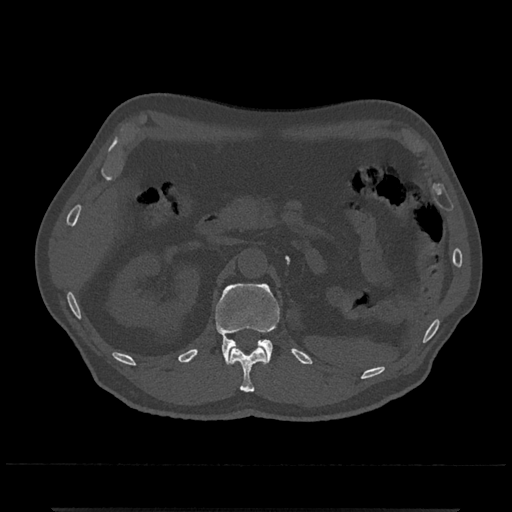
CT including the spine, one axial slice; slice 390 of 797 in the series (ordered by position); reconstruction kernel Br40s/3; 120 kVp; bone window (W 1800 / L 400 HU); 512 × 512 image matrix. Male patient, age 67 years. Case-level facts recorded for this patient, not image findings: primary cancer: prostate.
Annotated regions visible in this slice (semi-automatic segmentation, software-assisted and operator-edited):
- L1 vertebra: bounding box [x1, y1, x2, y2] px = [215, 283, 280, 365]
- T12 vertebra: [230, 346, 267, 393]